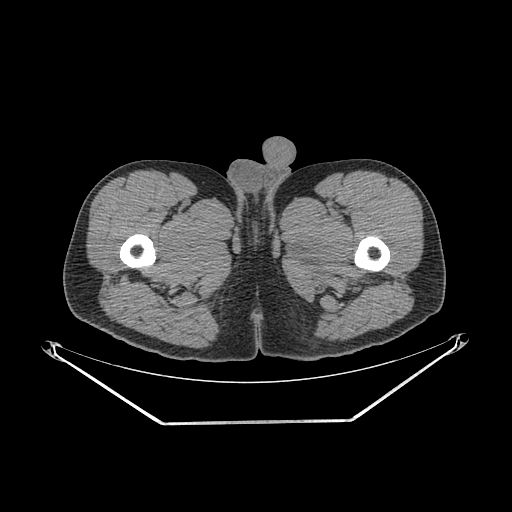
CT of an extremity soft-tissue mass (from a PET/CT study), one axial slice. 140 kVp. Soft-tissue window (W 400 / L 40 HU). 3.75 mm slice thickness. 512 × 512 image matrix. Male patient. Case-level facts recorded for this patient, not image findings: histological type: extraskeletal osteosarcoma; grade: high; site of the primary tumour: left adductur.
Outlined on this slice (expert contour drawn on MRI and transferred to this co-registered scan by the dataset authors):
- gross tumour volume (mass): bounding box [x1, y1, x2, y2] px = [283, 199, 385, 298]